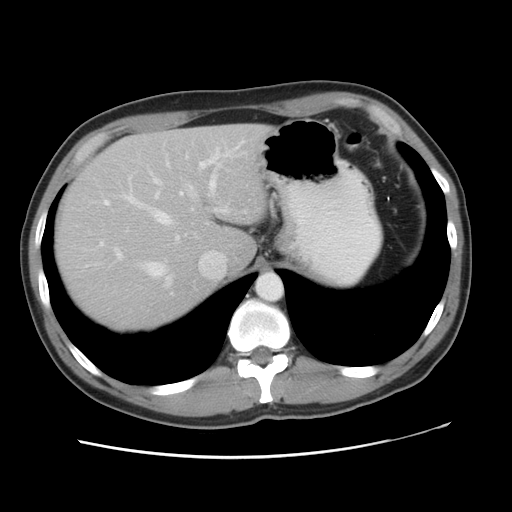
Contrast-enhanced abdominal CT, one axial slice; slice 37 of 49 in the series (ordered by position); reconstruction kernel STANDARD; intravenous contrast given; soft-tissue window (W 400 / L 40 HU); 5 mm slice thickness; 512 × 512 image matrix. Male patient, age 41 years. From the clinical record (not read from this slice): diagnosis: colorectal cancer liver metastases, imaged before liver resection; multiple liver metastases: yes; largest metastasis: 0.7 cm; disease in both lobes: yes.
Annotated regions visible in this slice (outlined manually by an expert reader):
- hepatic veins: bounding box <103,160,229,285> (left, top, right, bottom; pixels)
- liver: <54,126,265,331>
- planned liver remnant (the part of the liver to remain after resection): <100,126,266,269>
- portal vein (with intrahepatic branches): <100,148,228,257>